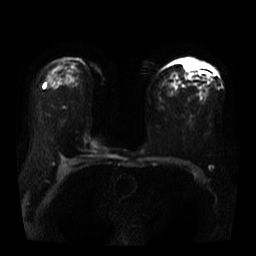
Breast MRI, one axial slice. Slice 23 of 40 in the series (ordered by position). Diffusion-weighted series; image 2 of 4 stored at this slice position (different b-values; order by instance number). 3 T. 256 × 256 image matrix, field of view 360 × 360 mm. Female patient.
Annotated regions visible in this slice (outlined manually by an expert reader):
- tumour on diffusion-weighted imaging: bounding box (x1, y1, x2, y2) in pixels: (185, 58, 195, 71)